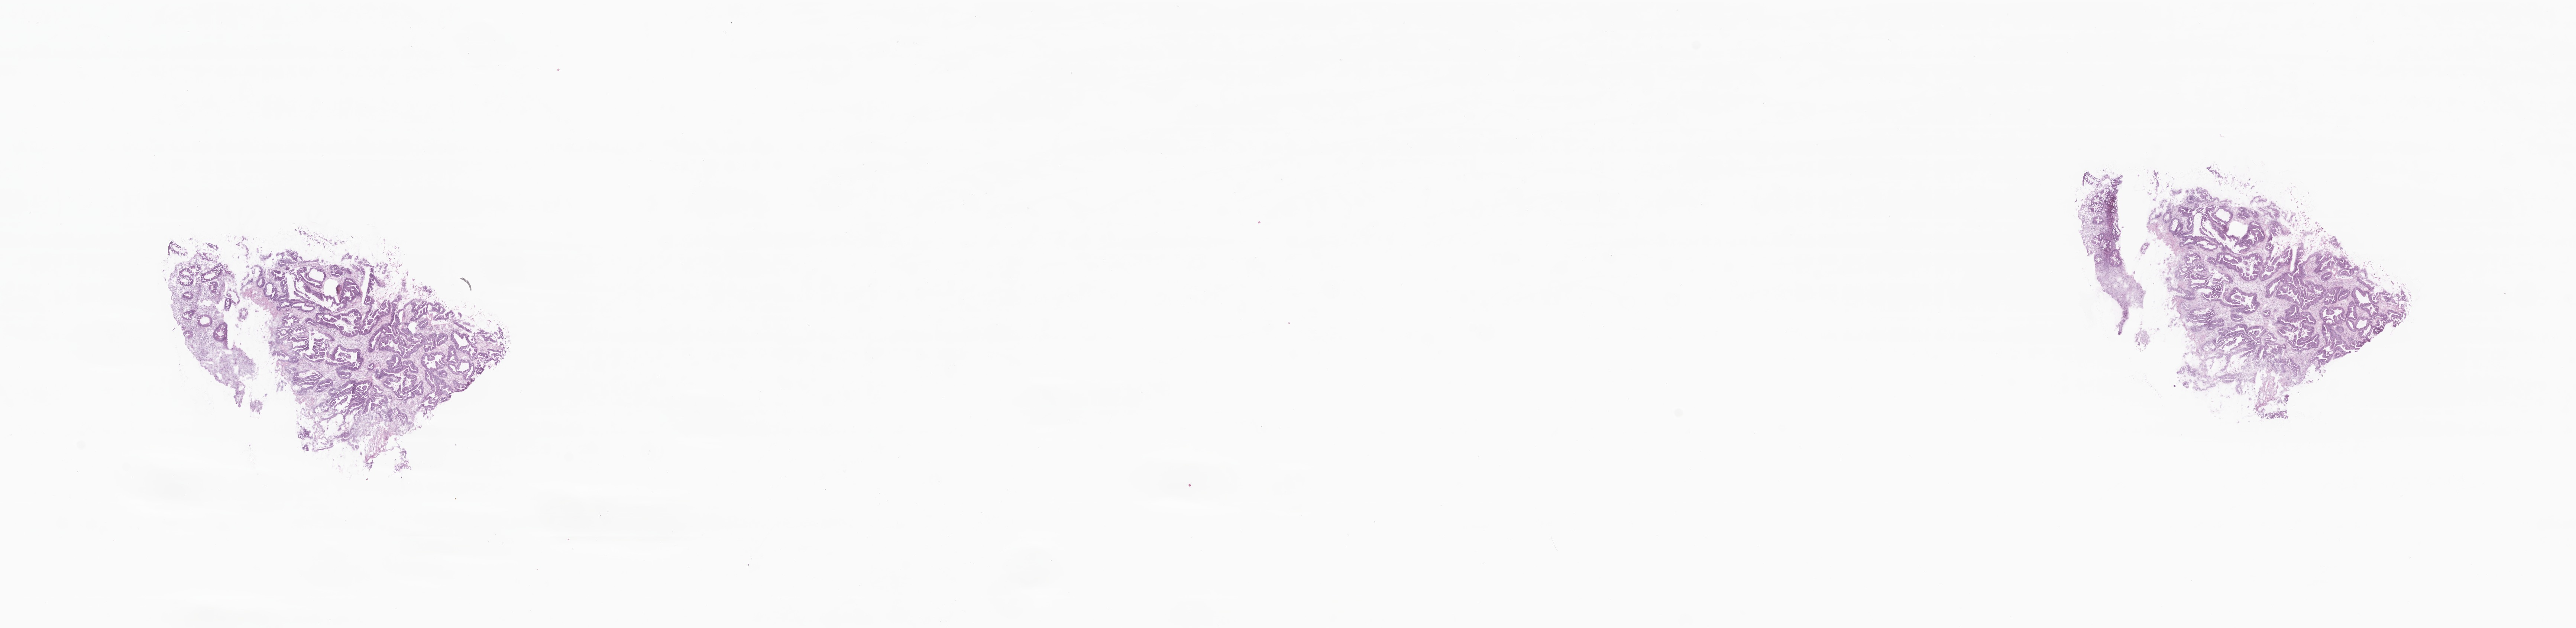
Whole-slide image, H&E stain — shown as a low-resolution overview of the whole scanned area (about 29.2 x 7.1 mm), frozen section, specimen: primary tumor, site: ileum. Female patient; age at initial diagnosis 83 years. Slide review estimates, as recorded: tumor cells 60%, tumor nuclei 60%, stromal cells 32%, necrosis 2%, normal cells 6%. Inflammatory infiltration, as recorded: lymphocyte infiltration 33%, monocyte infiltration 1%, neutrophil infiltration 0%.
Histologic diagnosis: Adenocarcinoma, NOS. Section: bottom of the tissue portion.